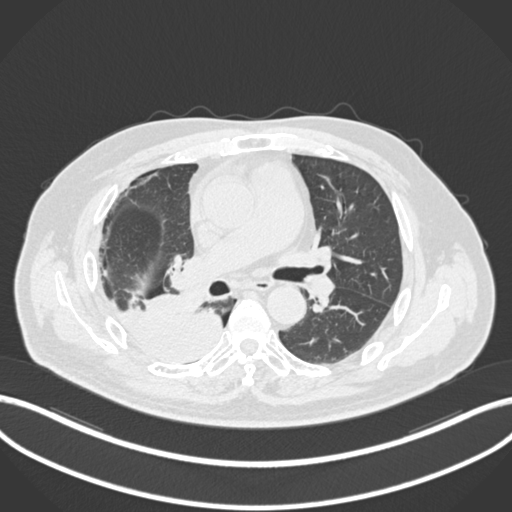
Chest CT, one axial slice; slice 107 of 218 in the series (ordered by position); 120 kVp; lung window (W 1500 / L -600 HU); 1 mm slice thickness; 512 × 512 image matrix, field of view 400 × 400 mm. Patient: male, 68 years. From the clinical record (not read from this slice): clinical TNM (as recorded): T2a N0 M0.
Structures marked on this image (bounding box drawn by a radiologist):
- lung tumour (recorded histology: adenocarcinoma): bounding box [x1, y1, x2, y2] px = [112, 290, 224, 362]